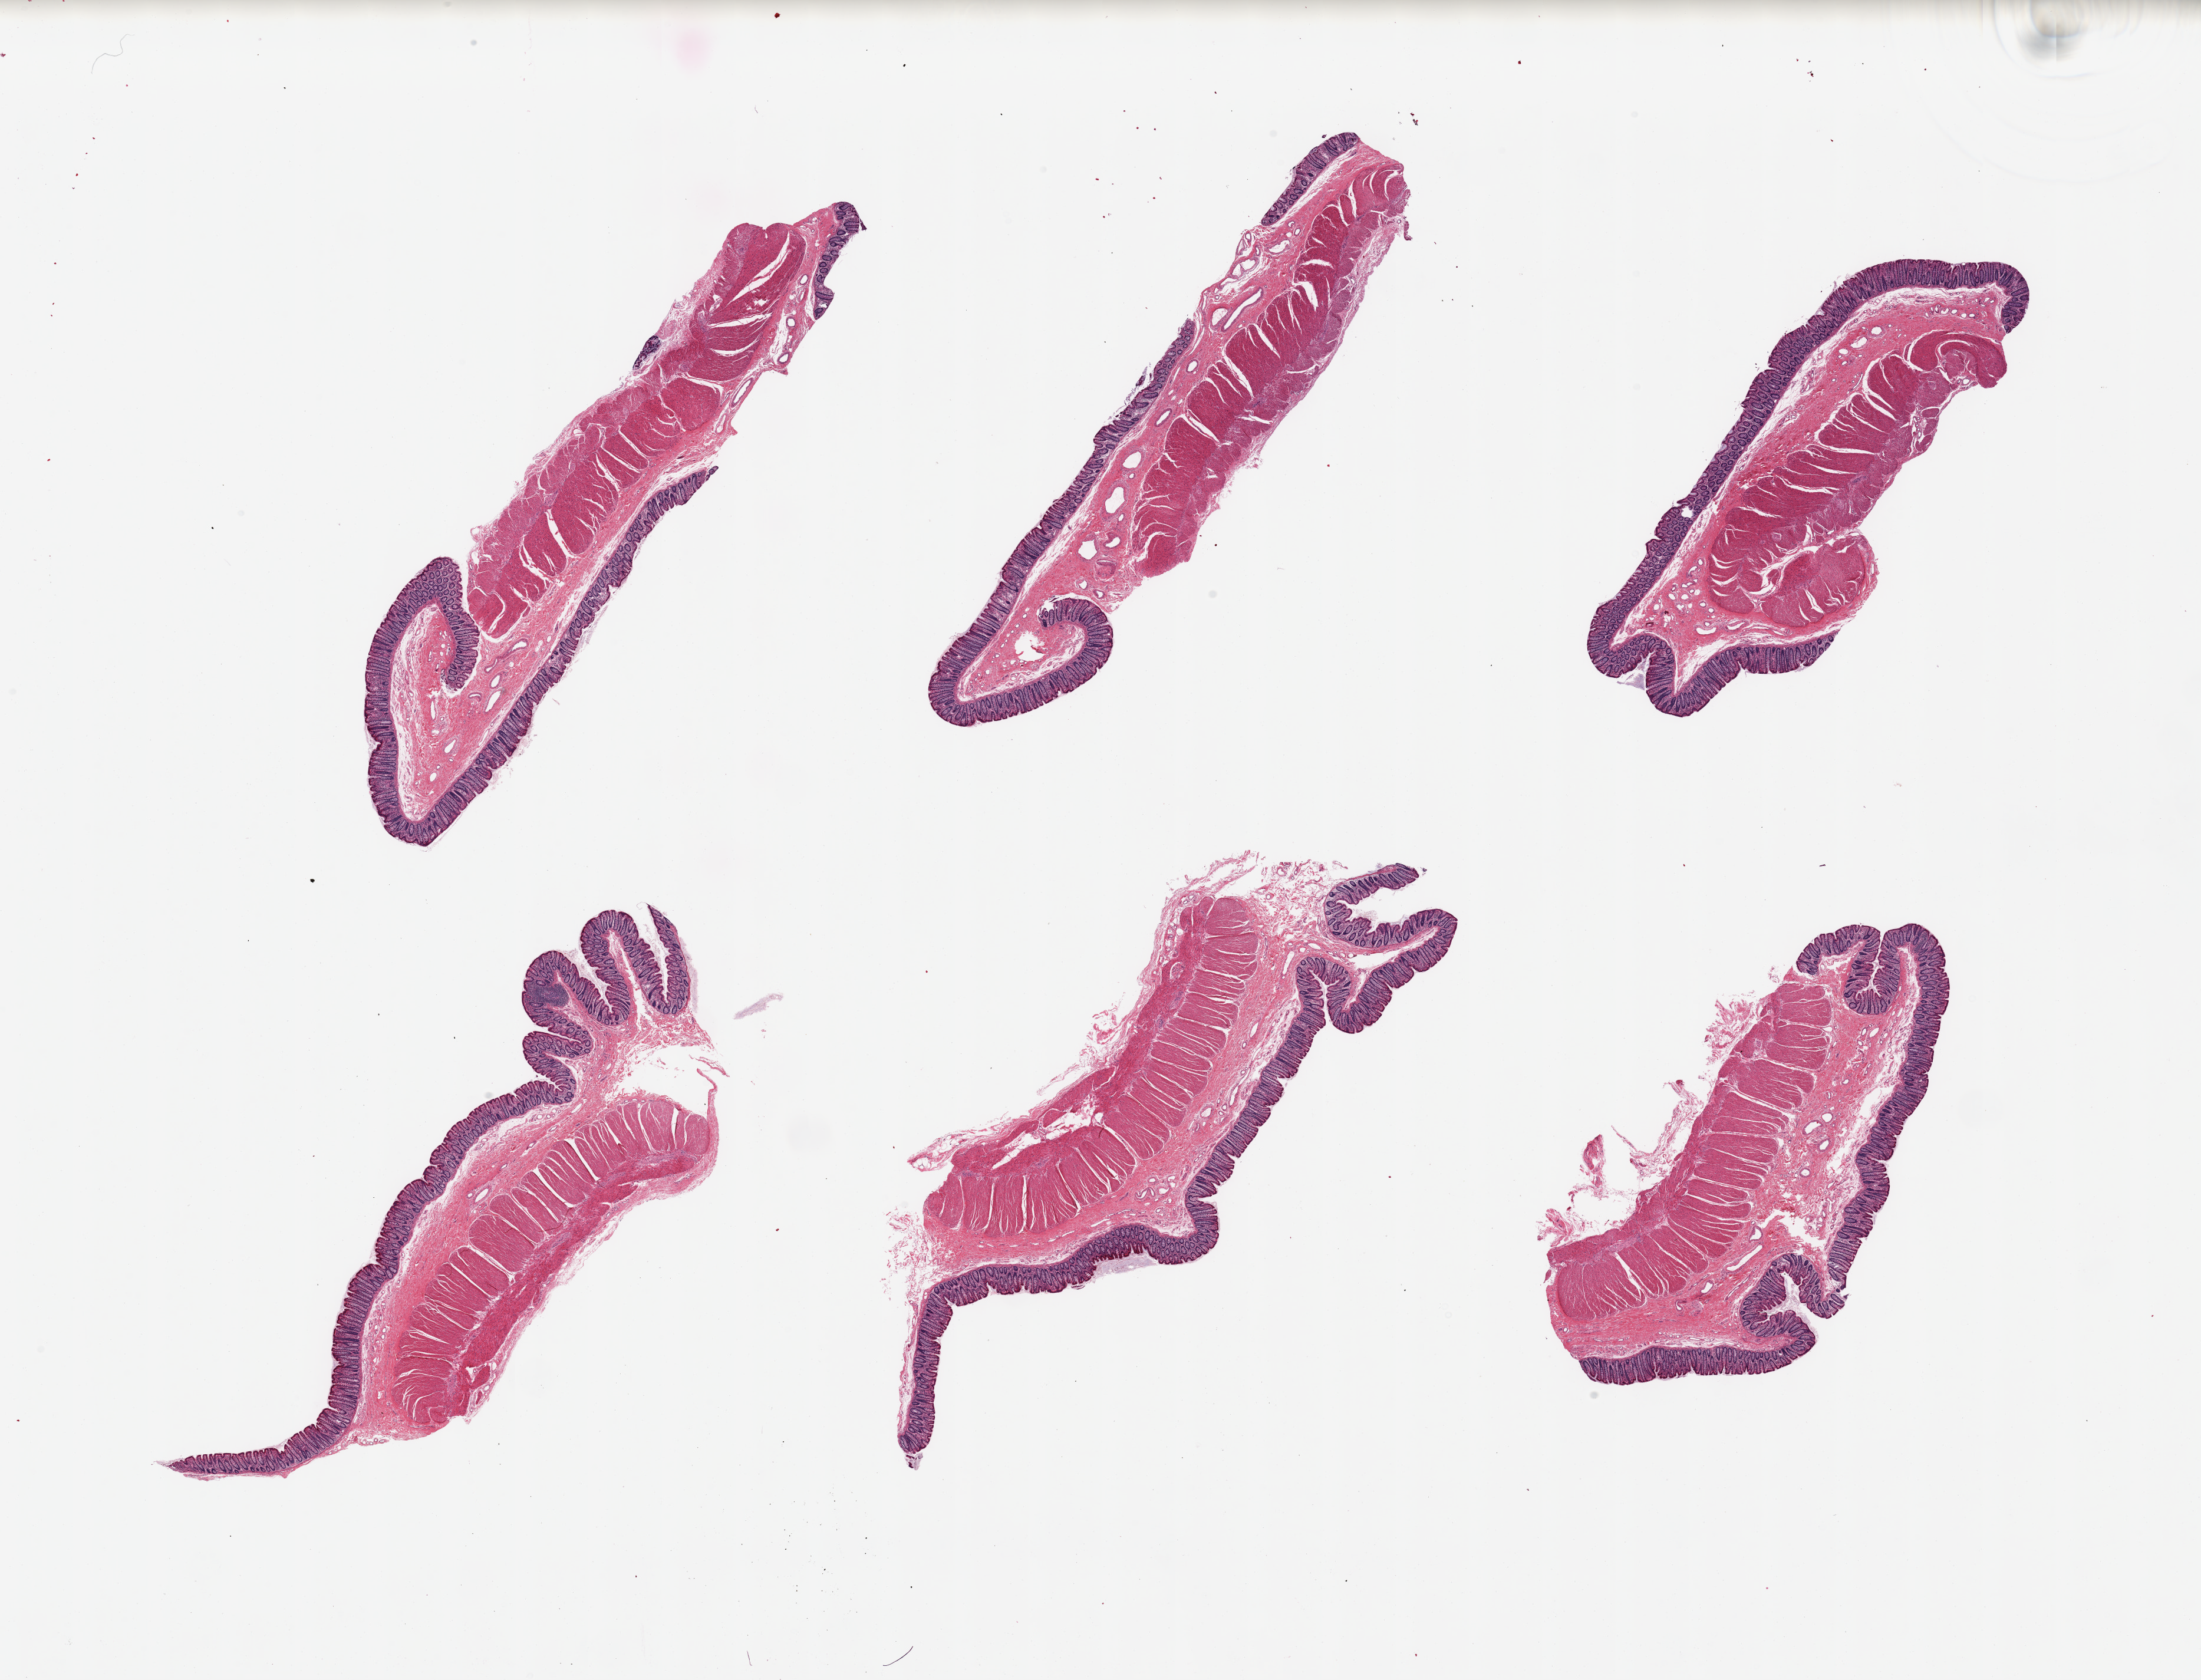
Digitized H&E-stained section — a low-resolution overview of the entire scanned area, about 29.5 x 22.5 mm. PAXgene-fixed paraffin-embedded (PFPE) section. Target tissue: transverse colon. Donor tissue sample. Male donor.
Pathologist's review note for this sample: 6 pieces; well preserved and dissected.